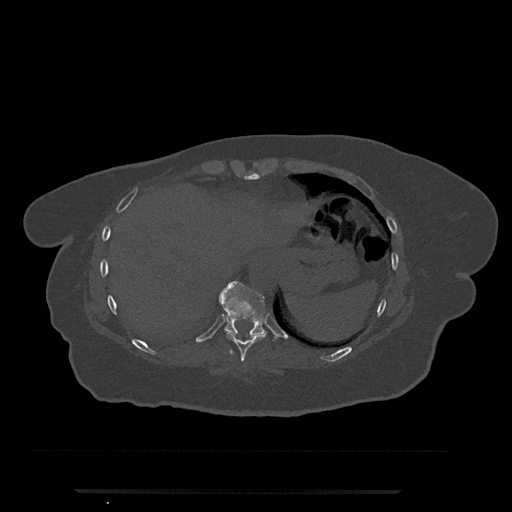
CT including the spine, one axial slice. Slice 314 of 797 in the series (ordered by position). Reconstruction kernel Br40s/3. 120 kVp. Bone window (W 1800 / L 400 HU). 0.5 mm slice thickness. 512 × 512 image matrix. Patient: female, 51 years. From the clinical record (not read from this slice): primary cancer: neuro; vertebrae with lytic lesions (as recorded): T8.
Structures marked on this image (semi-automatically segmented with operator editing):
- T10 vertebra: box from (x=219, y=281) to (x=267, y=338) px
- T9 vertebra: (x=226, y=332)–(x=267, y=362)